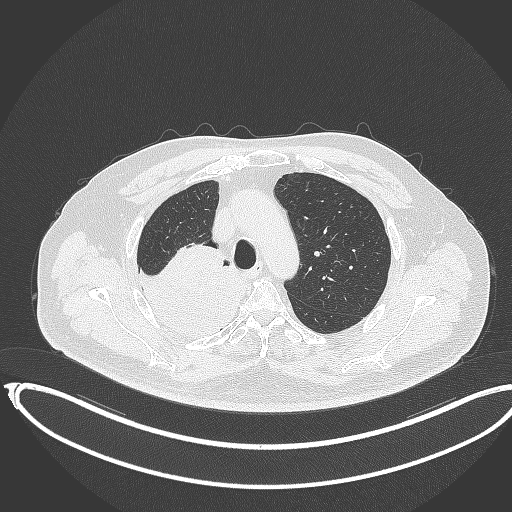
Chest CT, one axial slice; slice 277 of 403 in the series (ordered by position); reconstruction kernel B70f; 120 kVp; lung window (W 1500 / L -600 HU); 1 mm slice thickness; 512 × 512 image matrix, field of view 436 × 436 mm. Male patient, age 68 years. Case-level facts recorded for this patient, not image findings: clinical TNM (as recorded): T2a N0 M0.
Annotated regions visible in this slice (bounding box drawn by a radiologist):
- lung tumour (recorded histology: adenocarcinoma): bounding box [x1, y1, x2, y2] px = [131, 242, 254, 345]